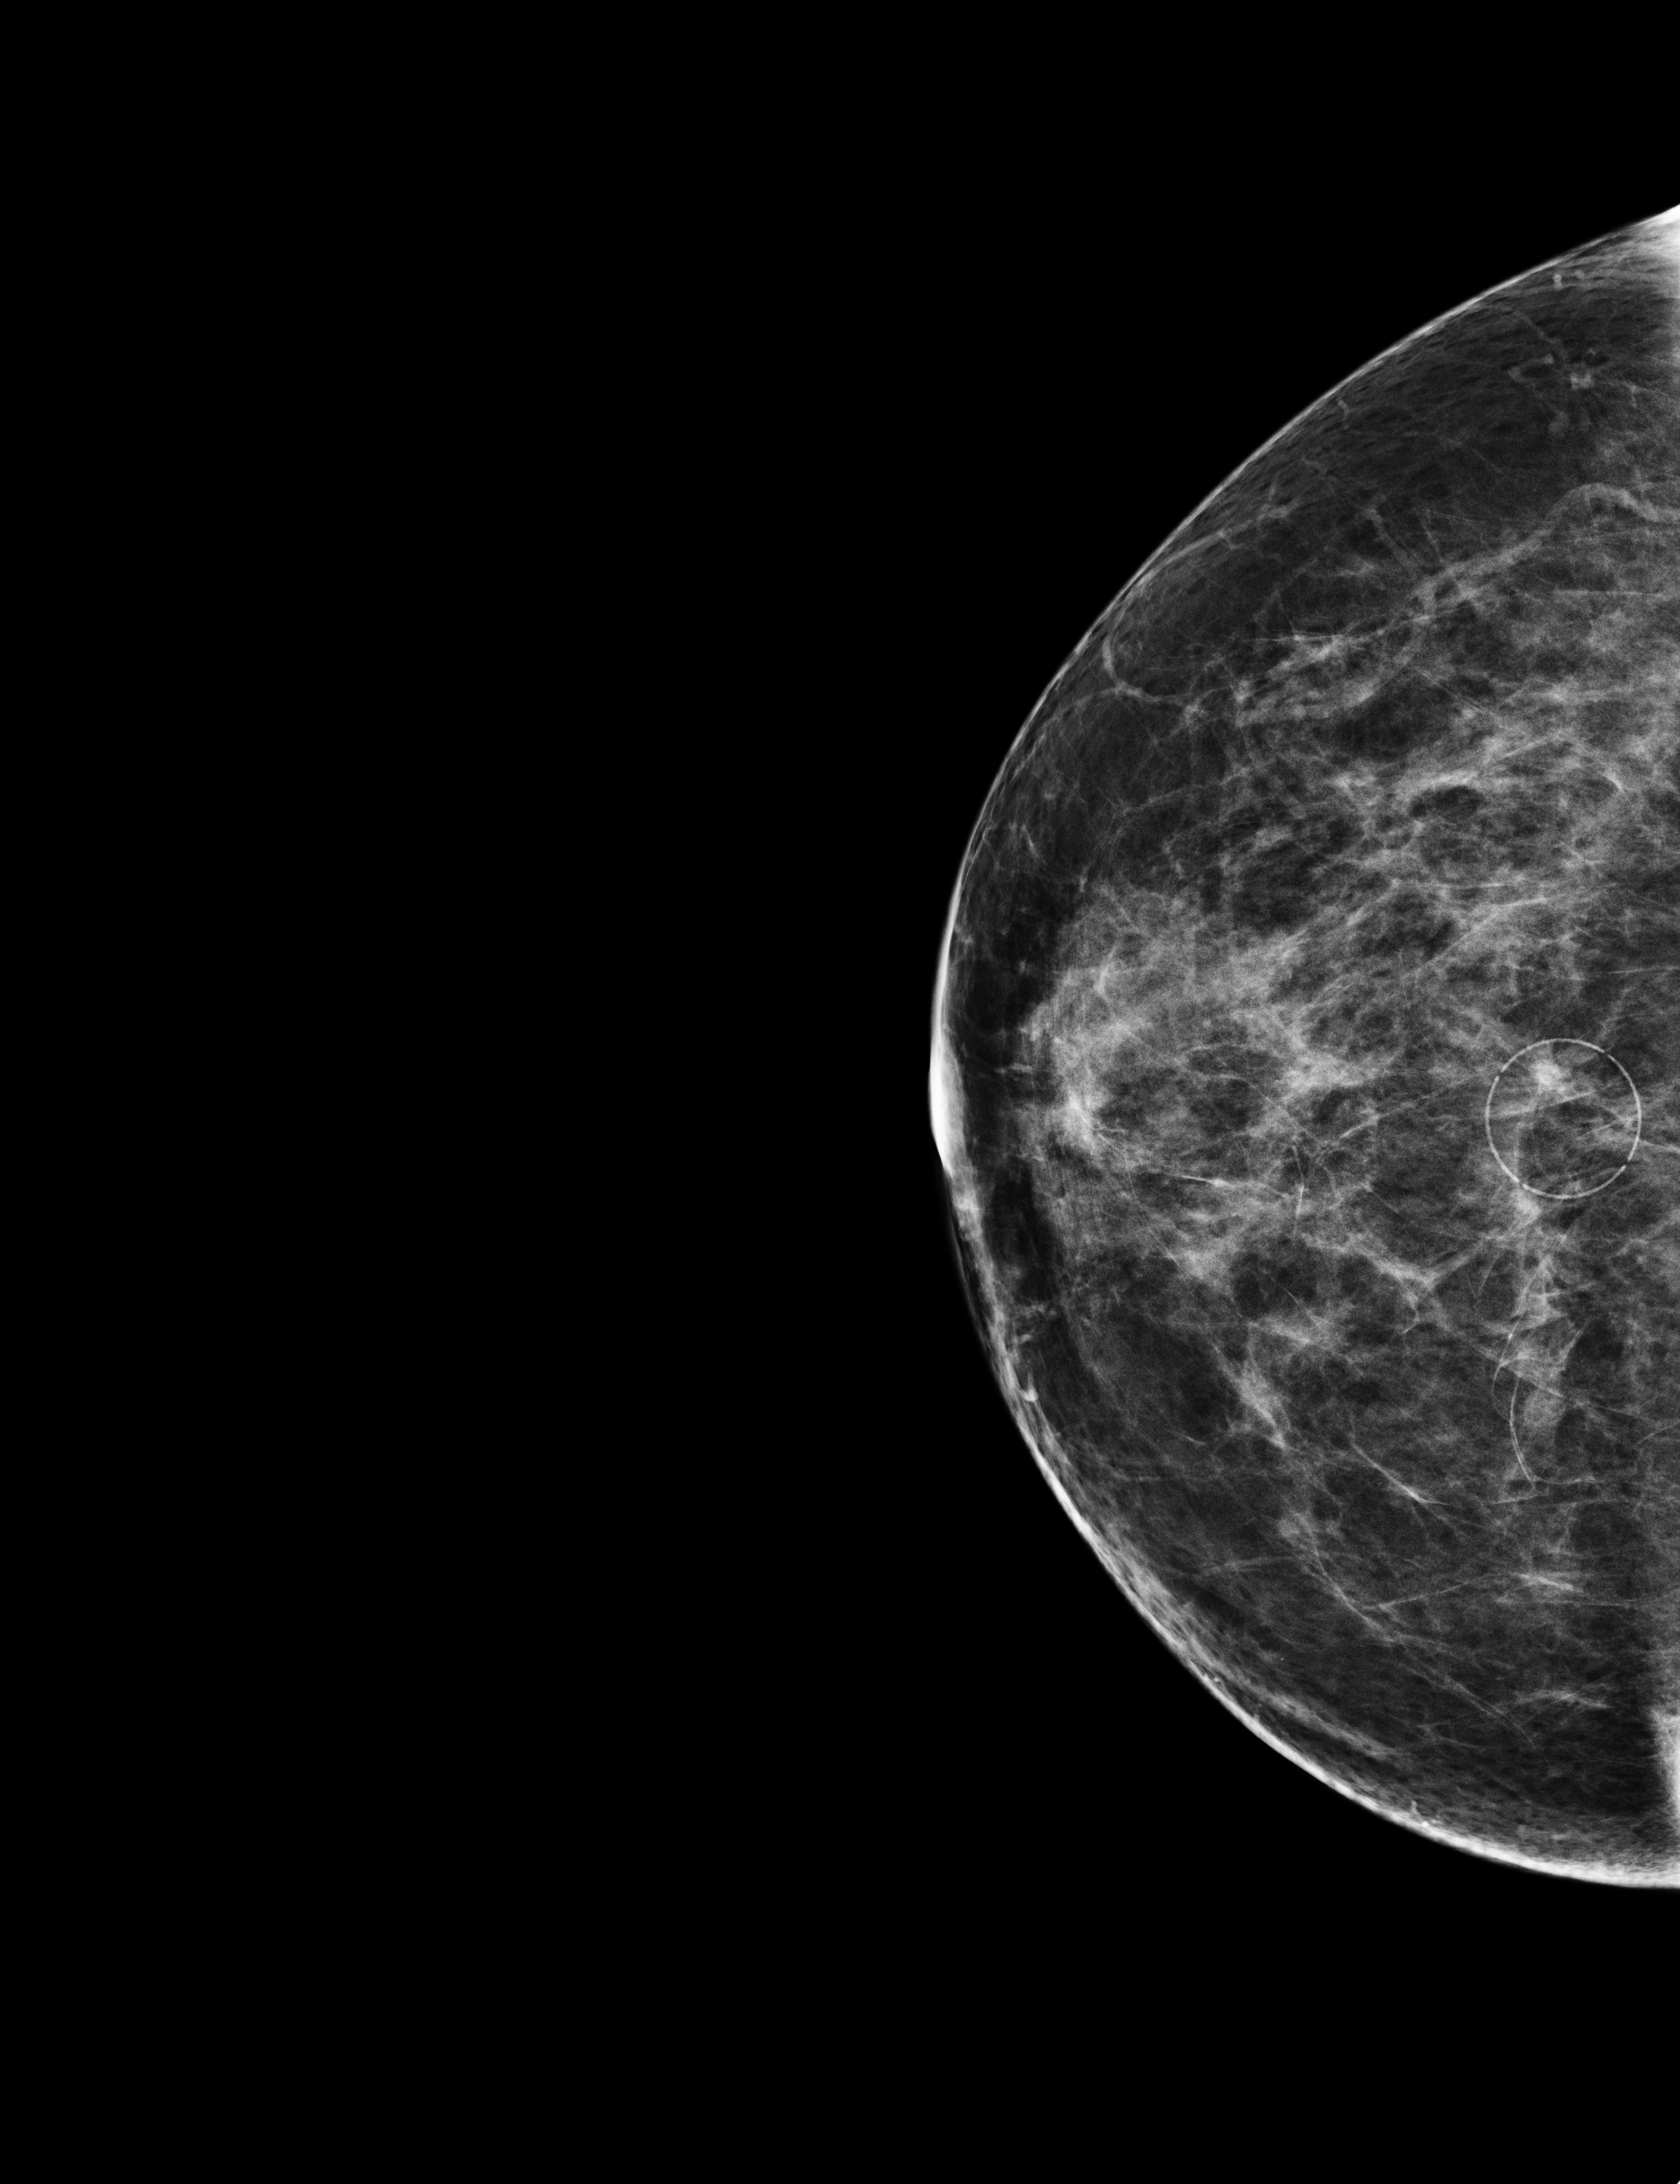
Screening examination, compressed breast thickness 54 mm, system: Selenia Dimensions. Patient: female, 61 years.
Image type: full-field digital mammogram. Breast: right. Projection: CC view.